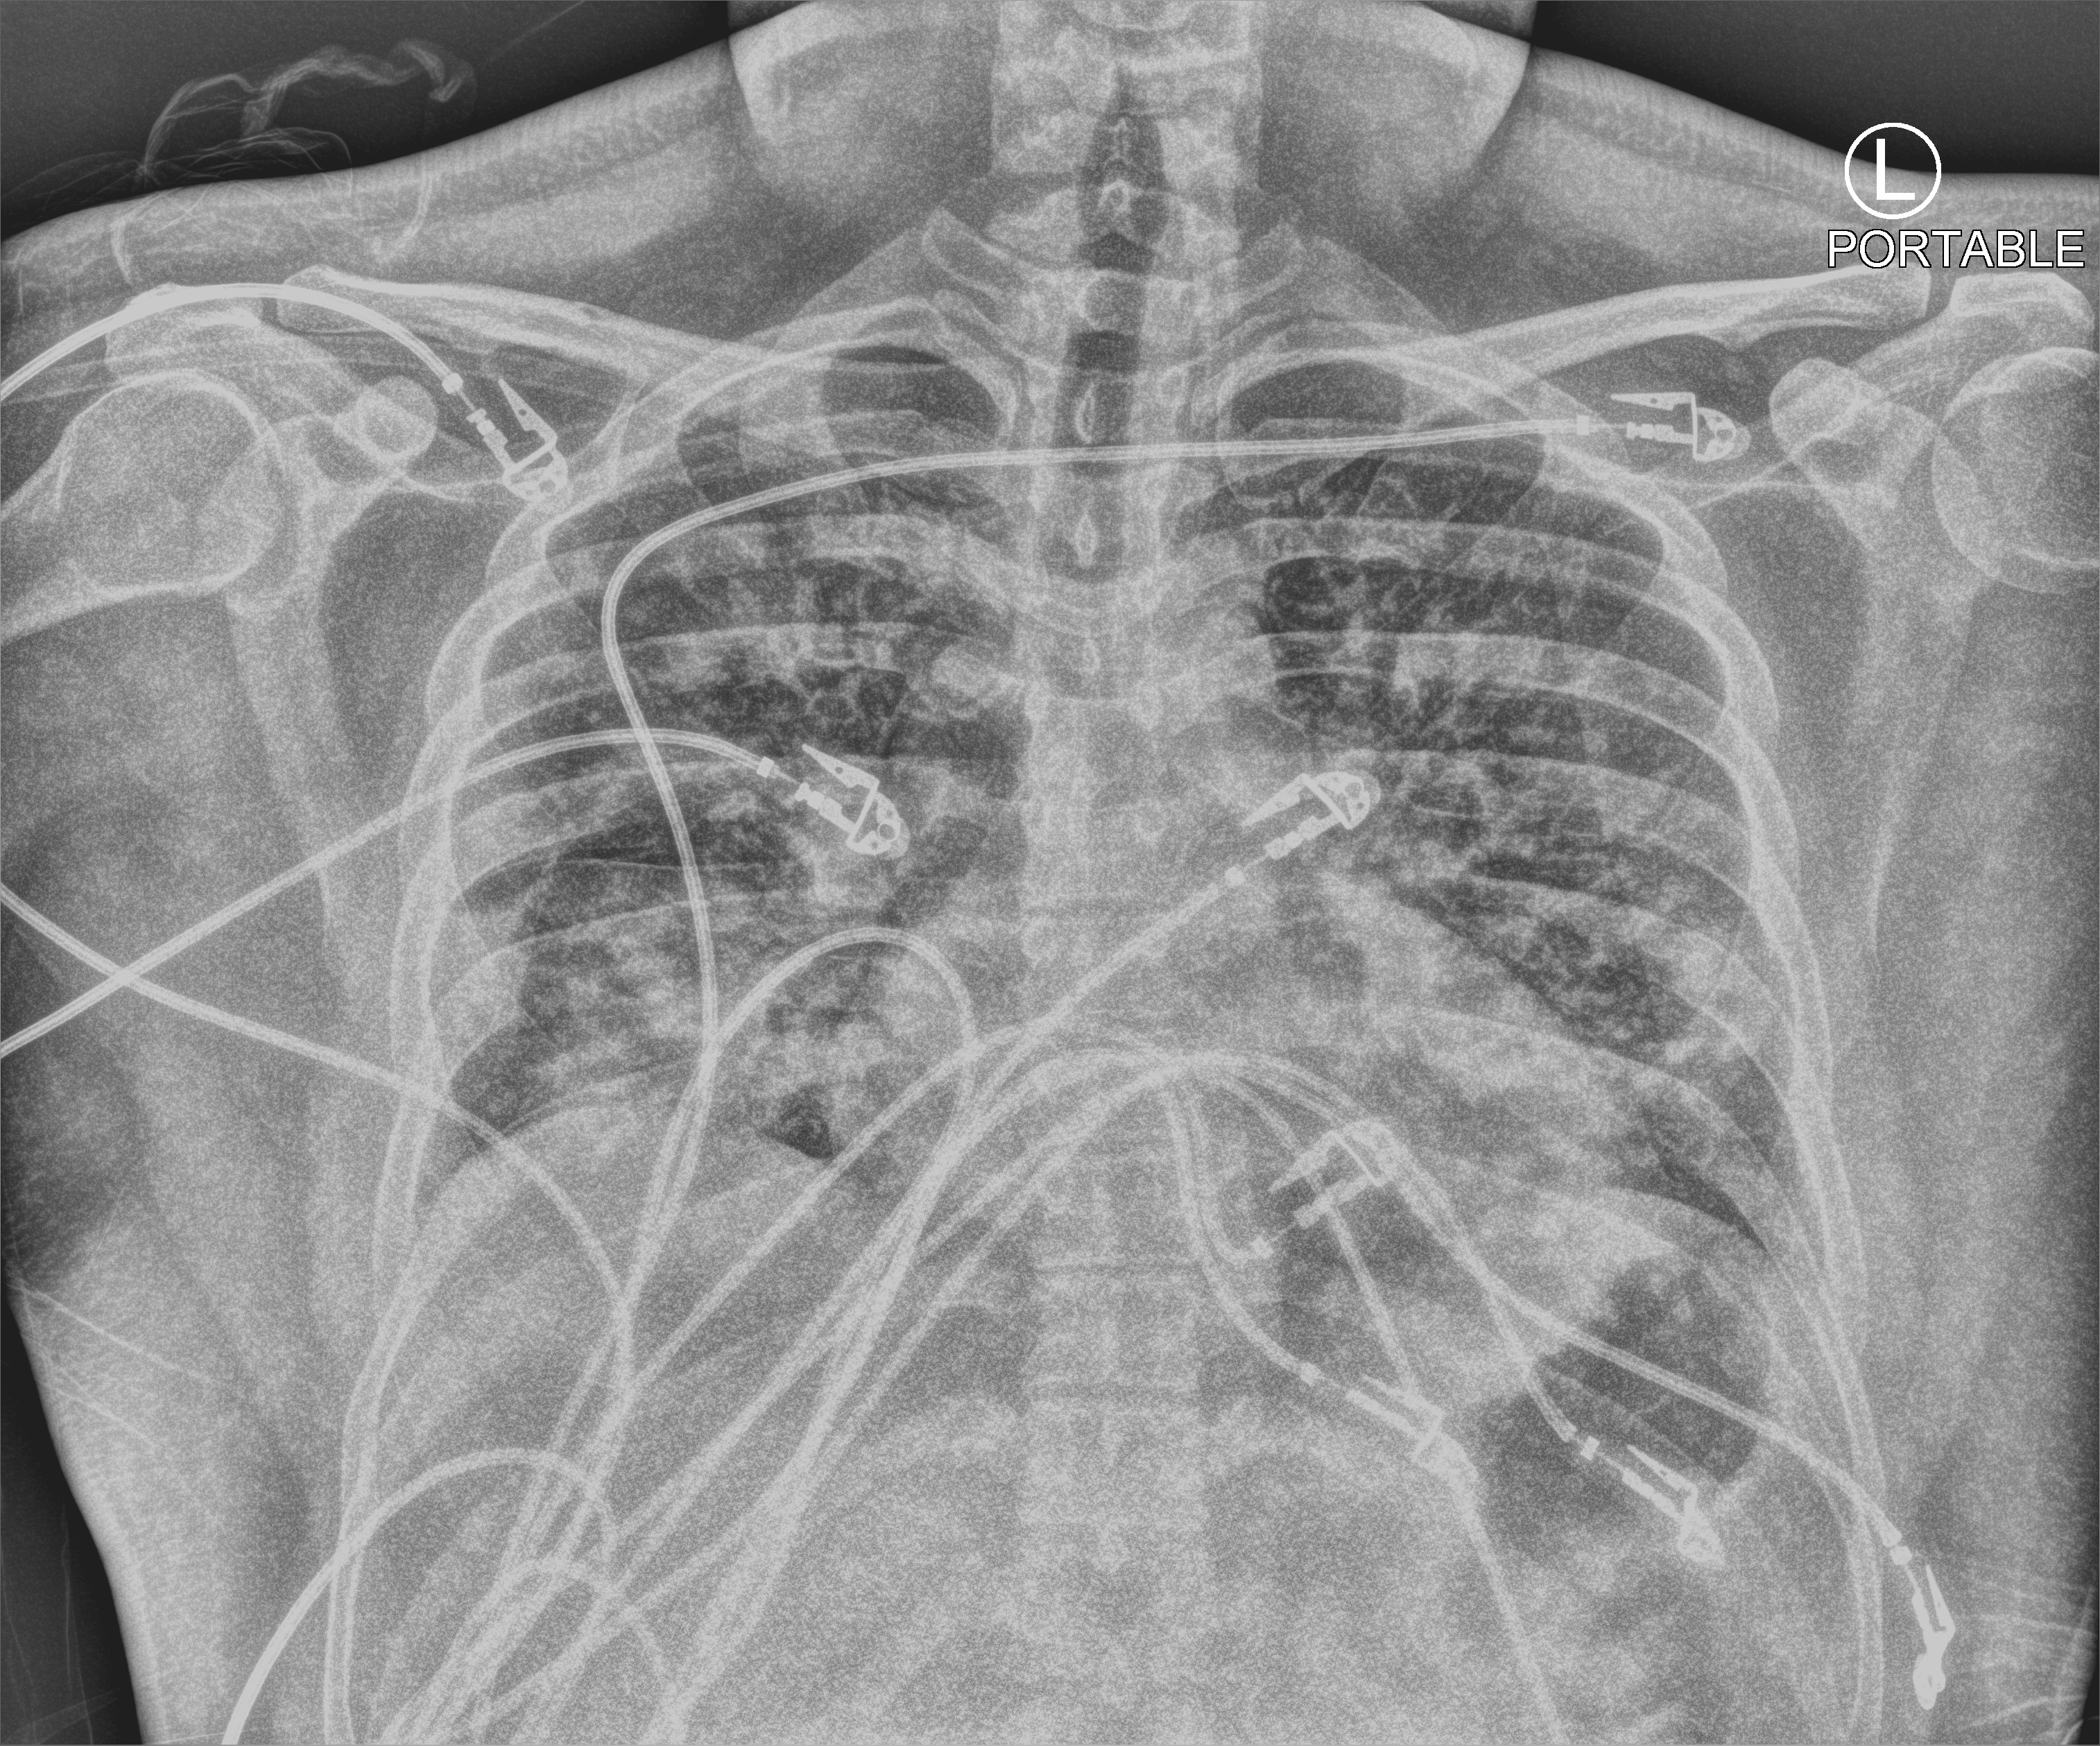
Portable chest radiograph. Male patient hospitalised with COVID-19, age 18–59 years.
Hospital-stay facts (about this admission, not read from this image; timing relative to this image not recorded): mechanically ventilated during this hospital stay: no; admitted to intensive care during this hospital stay: no.